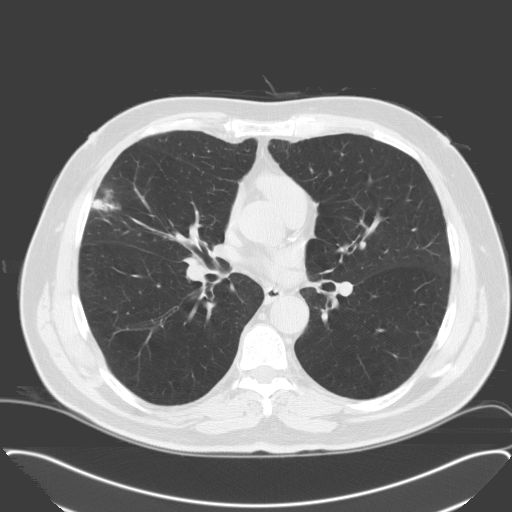
Low-dose screening chest CT, axial slice, third screening round (two years after baseline), lung window (W 1500 / L -600 HU), 3.2 mm slice thickness, 120 kVp, 512 × 512 image matrix. Male, age 65 years at enrolment.
Expert reader's lesion annotation, bounding box <76,185,129,237> (left, top, right, bottom; pixels). Screening reader's record for this exam (one nodule recorded; not confirmed to be the boxed lesion): non-calcified nodule or mass ≥4 mm, right middle lobe, 28 × 23 mm, spiculated (stellate) margins, soft tissue attenuation, pre-existing on the prior screen: no. Later outcome: lung cancer diagnosed 25 days after this screen — adenocarcinoma, NOS, right middle lobe, moderately differentiated (G2), stage IA (AJCC 6th edition), 25 mm at pathology.